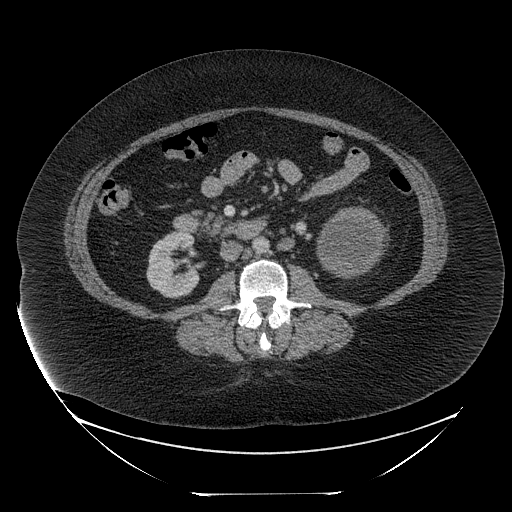
Contrast-enhanced abdominal CT, one axial slice. Position 113 of 205 along the scan axis. 120 kVp. Intravenous contrast given. Soft-tissue window (W 400 / L 40 HU). 2.5 mm slice thickness. 512 × 512 image matrix, field of view 500 × 500 mm. Female patient, age 53 years. Case-level facts recorded for this patient, not image findings: diagnosis: adrenocortical carcinoma; tumour side: left adrenal; tumour size at pathology: 17 cm; Ki-67 index: 20 %; stage (as recorded): 3.
Structures marked on this image (semi-automatic segmentation, software-assisted and operator-edited):
- mass: bounding box <319,209,383,276> (left, top, right, bottom; pixels)